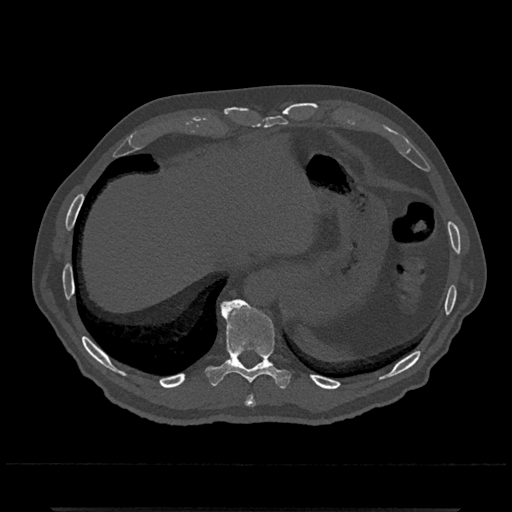
CT including the spine, one axial slice; position 554 of 797 along the scan axis; bone window (W 1800 / L 400 HU); 512 × 512 image matrix. Patient: male, 67 years. From the clinical record (not read from this slice): primary cancer: prostate.
Structures marked on this image (semi-automatically segmented with operator editing):
- T10 vertebra: bounding box [x1, y1, x2, y2] px = [205, 299, 291, 389]
- T9 vertebra: [245, 395, 256, 407]